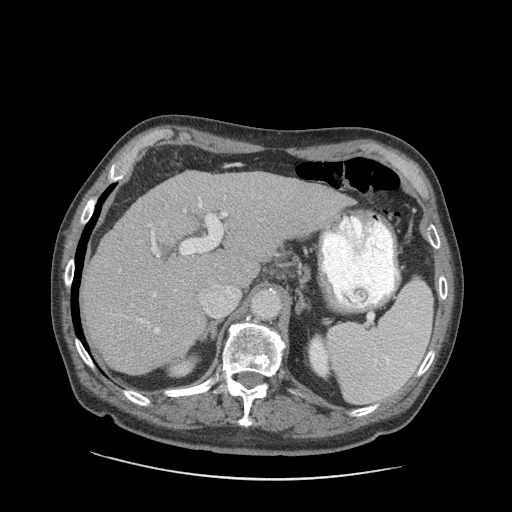
Contrast-enhanced abdominal CT (liver protocol), one axial slice. Slice 59 of 89 in the series (ordered by position). Soft-tissue window (W 400 / L 40 HU). 2.5 mm slice thickness. 512 × 512 image matrix. Case-level facts recorded for this patient, not image findings: diagnosis: hepatocellular carcinoma (patient treated with transarterial chemoembolisation; whether this scan precedes or follows treatment is not stated here); TNM stage (as recorded): Stage-I; Child-Pugh class: A; tumour differentiation: moderately differentiated; tumour size: 4.6 cm.
Structures marked on this image (semi-automatically segmented with operator editing):
- liver parenchyma outside the tumour (the mass and vessels are separate outlines, so this box may not span the whole liver): bounding box [x1, y1, x2, y2] px = [82, 170, 352, 374]
- liver vessels: [117, 189, 334, 334]